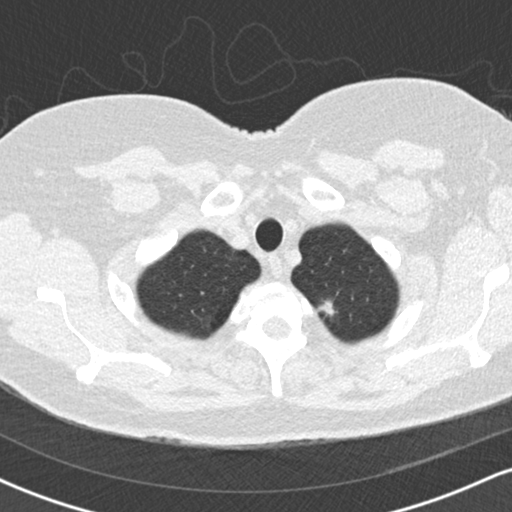
Low-dose screening chest CT, one axial slice. Slice 150 of 170 in the series (ordered by position). 120 kVp. Lung window (W 1500 / L -600 HU). 2 mm slice thickness. 512 × 512 image matrix.
Structures marked on this image (outlined manually by an expert reader):
- lesion 1 (tumor, upper lobe of left lung): bounding box <319,302,334,315> (left, top, right, bottom; pixels)